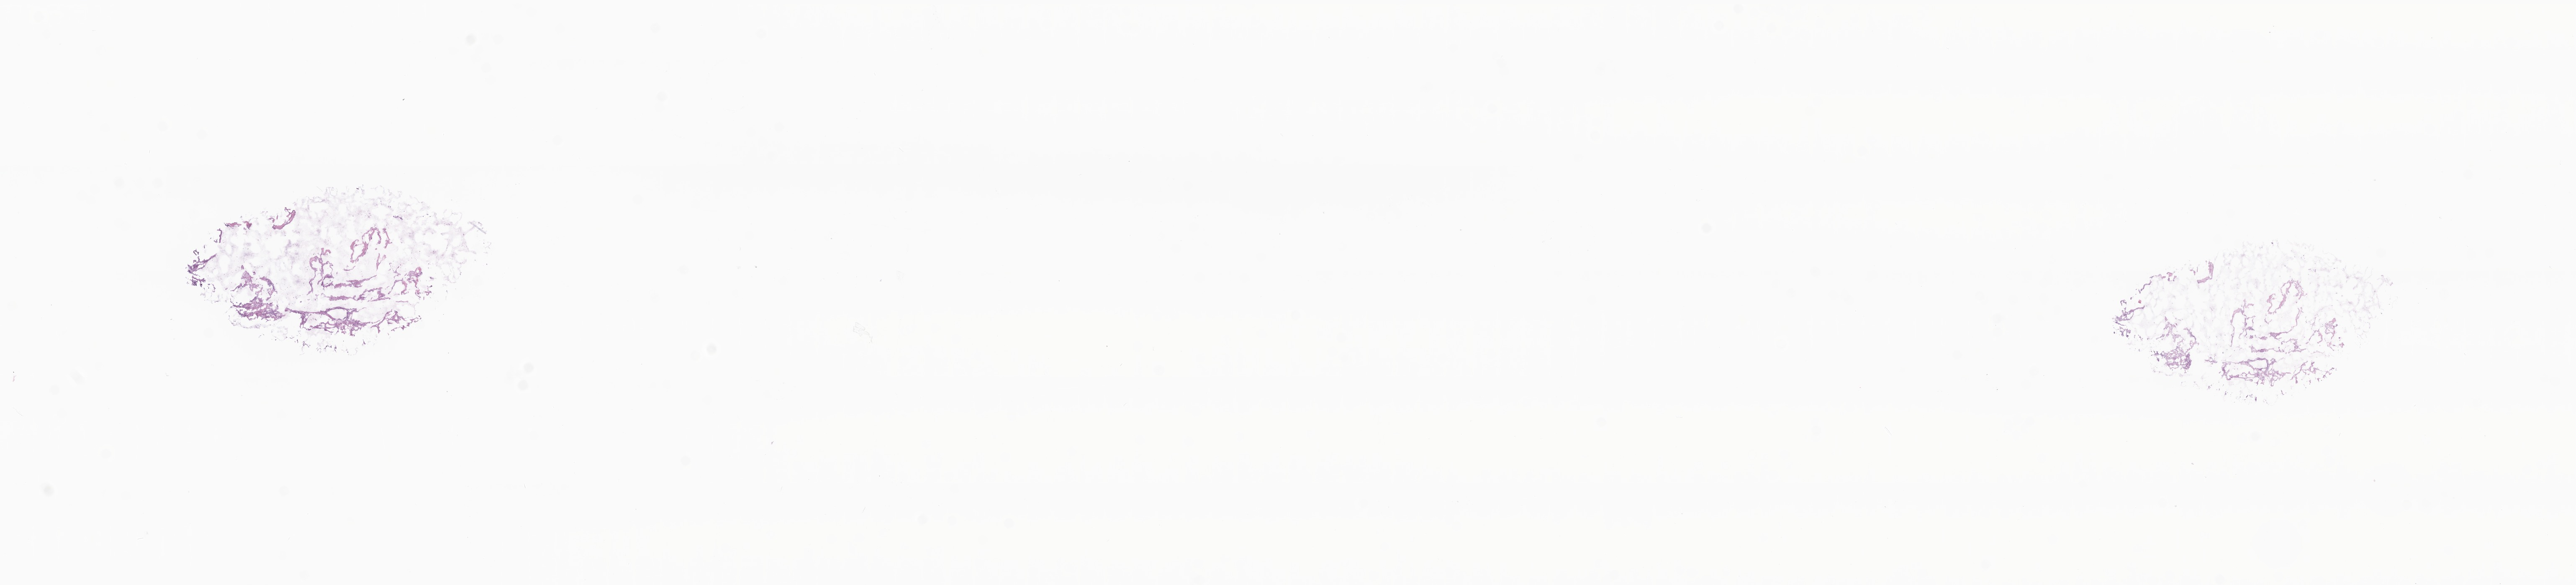
Whole-slide image, H&E stain — whole scanned area (about 26.0 x 5.9 mm) shown as a low-resolution overview. Cryosection. Specimen: metastatic tumor tissue. Male patient; age at initial diagnosis 63 years. Composition of this section per pathologist review: tumor cells 15%, tumor nuclei 25%.
Patient diagnosis (primary): Mucinous adenocarcinoma.